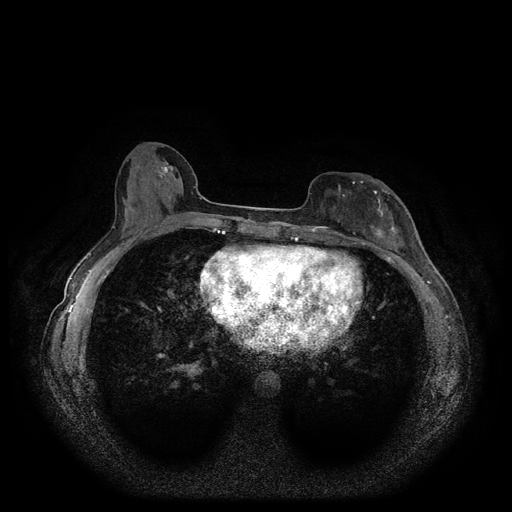
Breast MRI (dynamic contrast-enhanced, multi-phase), one axial slice; slice 45 of 116 in the series (ordered by position); dynamic contrast-enhanced series, time point 2 of 5 at this slice position (early post-contrast); 1.5 T; TE 2.6 ms, TR 5.3 ms; 2 mm slice thickness; 512 × 512 image matrix, field of view 350 × 350 mm. Patient: female, 51 years.
Outlined on this slice (semi-automatically segmented with operator editing):
- breast lesion (labelled 'tumour' in the annotation; benign lesions carry a separate 'benign' label): bounding box (x1, y1, x2, y2) in pixels: (364, 197, 400, 248)
- breast lesion (labelled benign in the annotation): (155, 160, 178, 179)